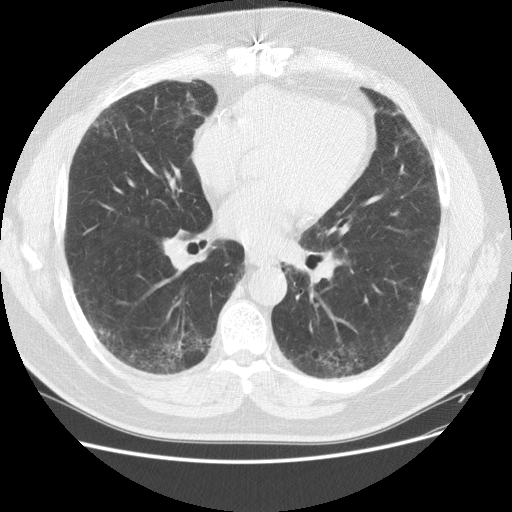
Low-dose screening chest CT, axial slice. Baseline screening round. Lung window (W 1500 / L -600 HU). 2.5 mm slice thickness. Male, age 59 years at enrolment.
Lesion marked by an expert reader, bounding box <82,98,132,148> (left, top, right, bottom; pixels). The screening reader recorded 2 non-calcified nodules or masses ≥4 mm on this exam; which of them this box marks is not recorded. Participant outcome: lung cancer diagnosed 338 days after this screen — adenocarcinoma, NOS, right upper lobe, right middle lobe, moderately differentiated (G2), stage IA (AJCC 6th edition), 13 mm at pathology.